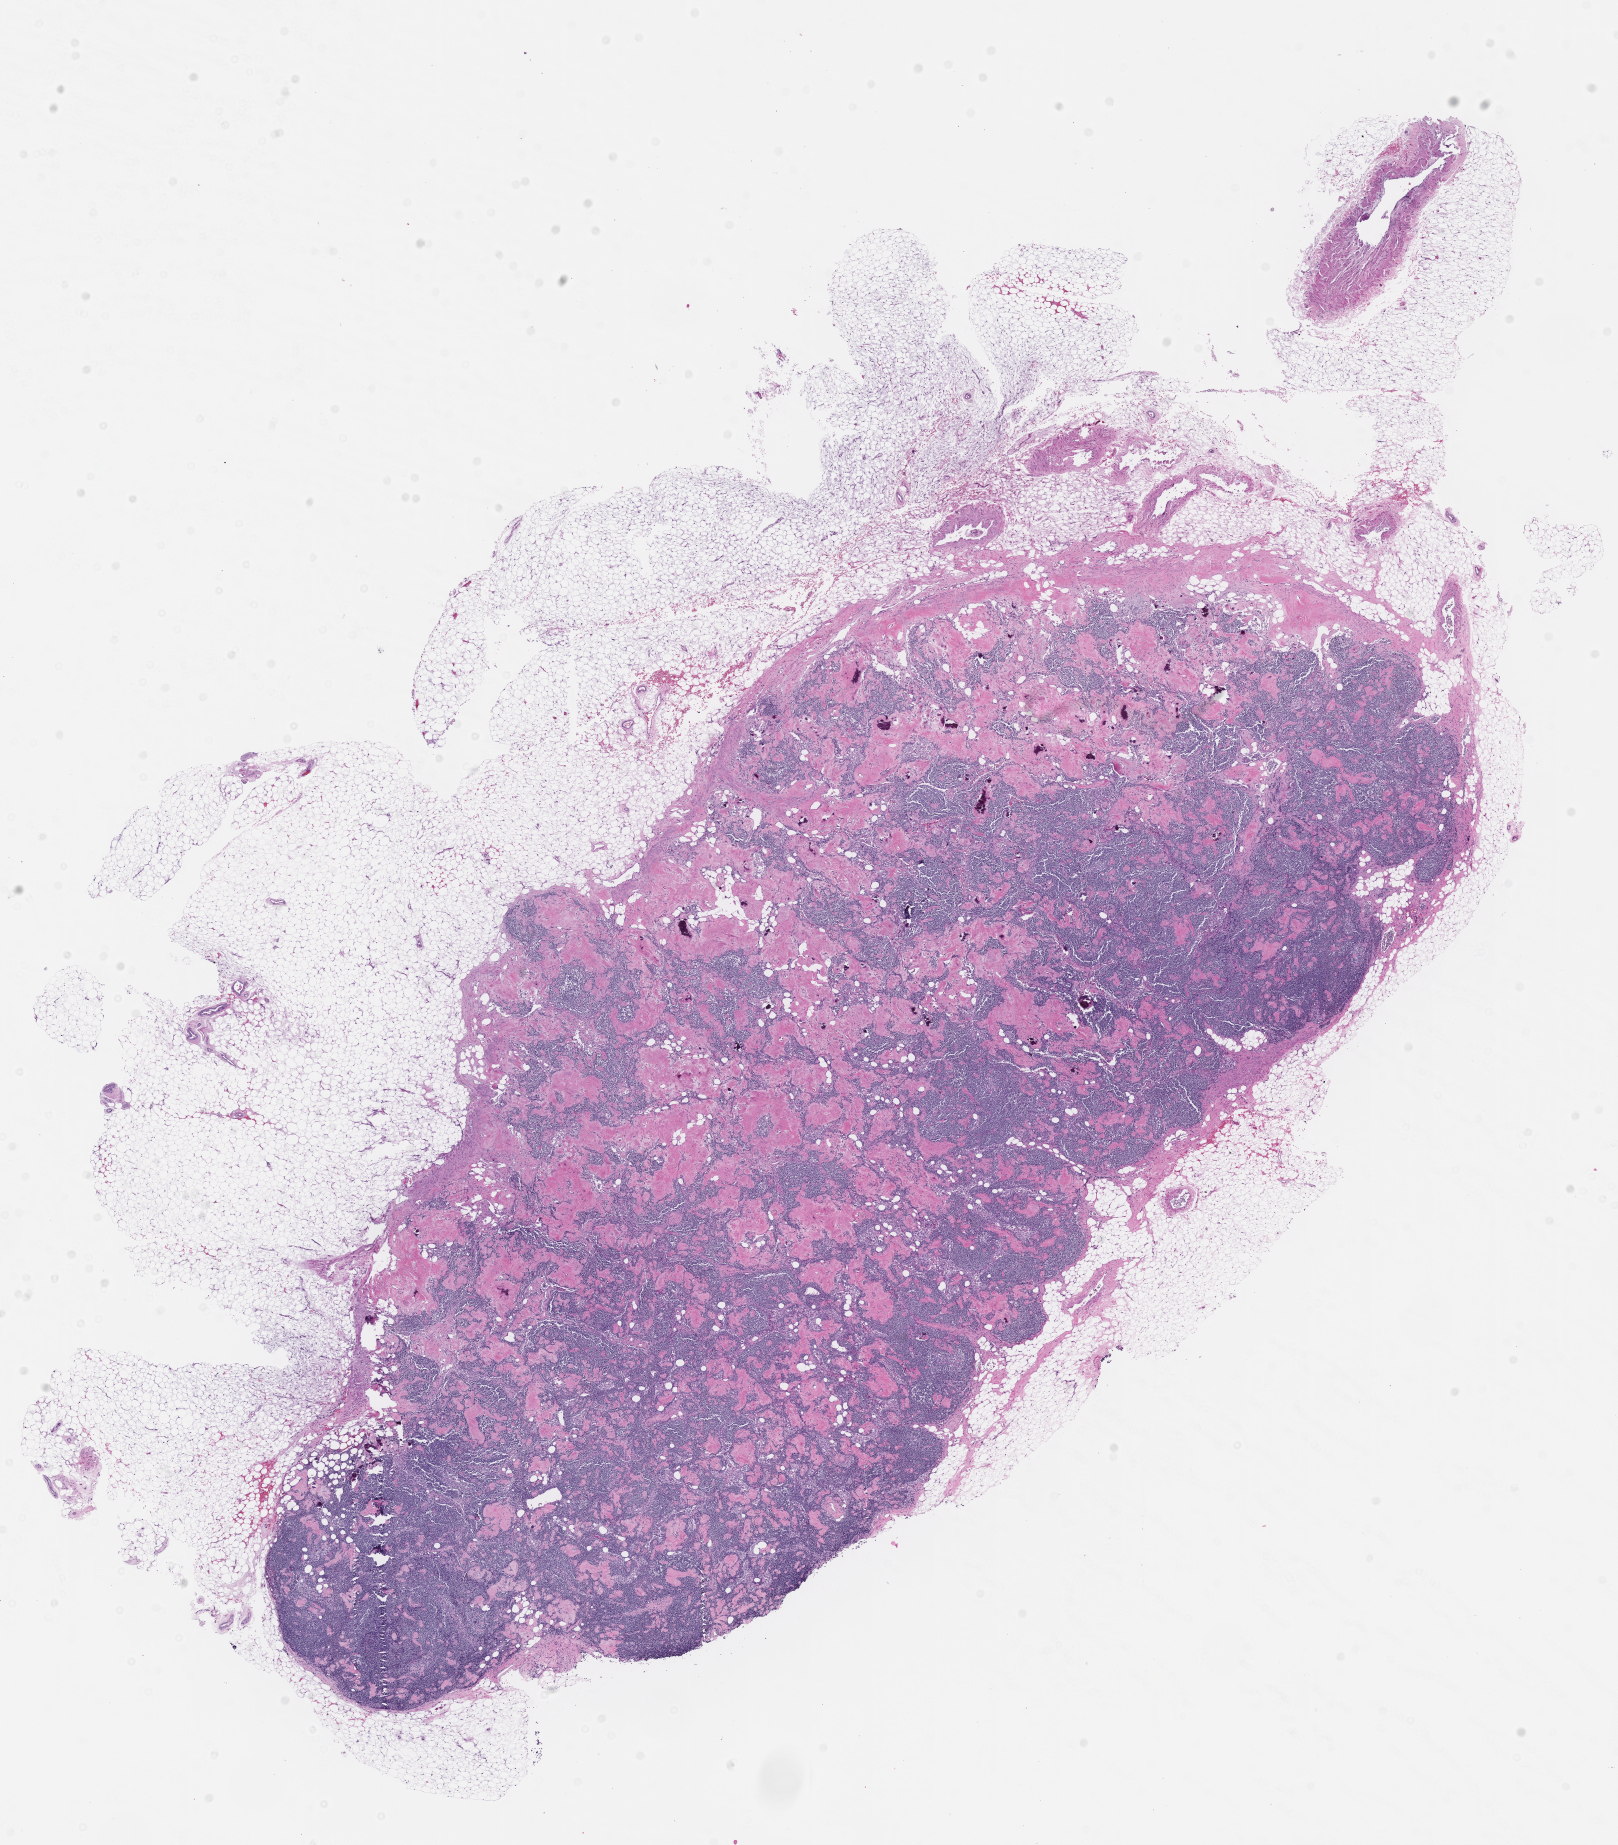
H&E whole-slide image — a low-resolution overview of the entire scanned area, about 13.1 x 14.9 mm. Formalin-fixed paraffin-embedded section. Specimen: non-tumor (normal tissue) sample from a patient with papillary urothelial carcinoma. Site: bladder. Patient: male, age at initial diagnosis 84 years. Slide review estimates, as recorded: tumor cells 0%, tumor nuclei 0%, stromal cells 100%, necrosis 0%, normal cells 0%. Infiltration values recorded for this section: lymphocyte infiltration 100%, monocyte infiltration 0%, neutrophil infiltration 0%.
This section: non-tumor tissue sample; the patient's diagnosis is given above. Section: bottom of the tissue portion.